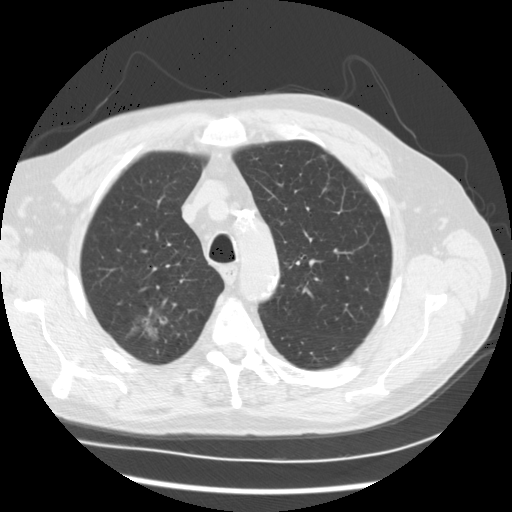
Axial slice from a low-dose chest CT screening exam; first (baseline) screen; lung window (W 1500 / L -600 HU); 2.5 mm slice thickness; standard (soft-tissue) reconstruction kernel (STANDARD); 120 kVp; 512 × 512 image matrix, field of view 360 × 360 mm. Male participant, aged 68 years at enrolment. Current smoker at enrolment.
• Expert reader's lesion annotation, bounding box <113,291,188,363> (left, top, right, bottom; pixels).
• The screening reader recorded 3 non-calcified nodules or masses ≥4 mm on this exam (right upper lobe, right upper lobe, right lower lobe); which of them this box marks is not recorded.
• Official screen result: positive, change unspecified: nodule(s) >= 4 mm or enlarging nodule(s), mass(es), or other non-specific abnormalities suspicious for lung cancer.
• Later outcome: lung cancer diagnosed 90 days after this screen — adenocarcinoma, NOS, right upper lobe, right lower lobe, well differentiated (G1), stage IV (AJCC 6th edition), 35 mm at pathology.